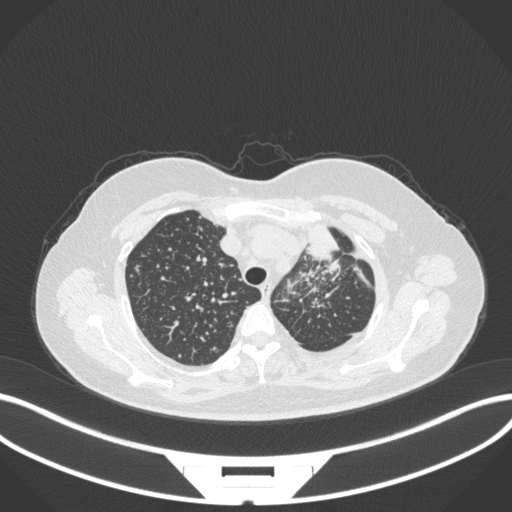
Chest CT, one axial slice; position 267 of 348 along the scan axis; reconstruction kernel B31f; 120 kVp; lung window (W 1500 / L -600 HU); 1 mm slice thickness; 512 × 512 image matrix, field of view 400 × 400 mm. Female patient, age 49 years. From the clinical record (not read from this slice): clinical TNM (as recorded): T1c N0 M1.
Annotated regions visible in this slice (rectangle marked by the reading radiologist):
- lung tumour (recorded histology: adenocarcinoma): bounding box (x1, y1, x2, y2) in pixels: (307, 218, 340, 261)